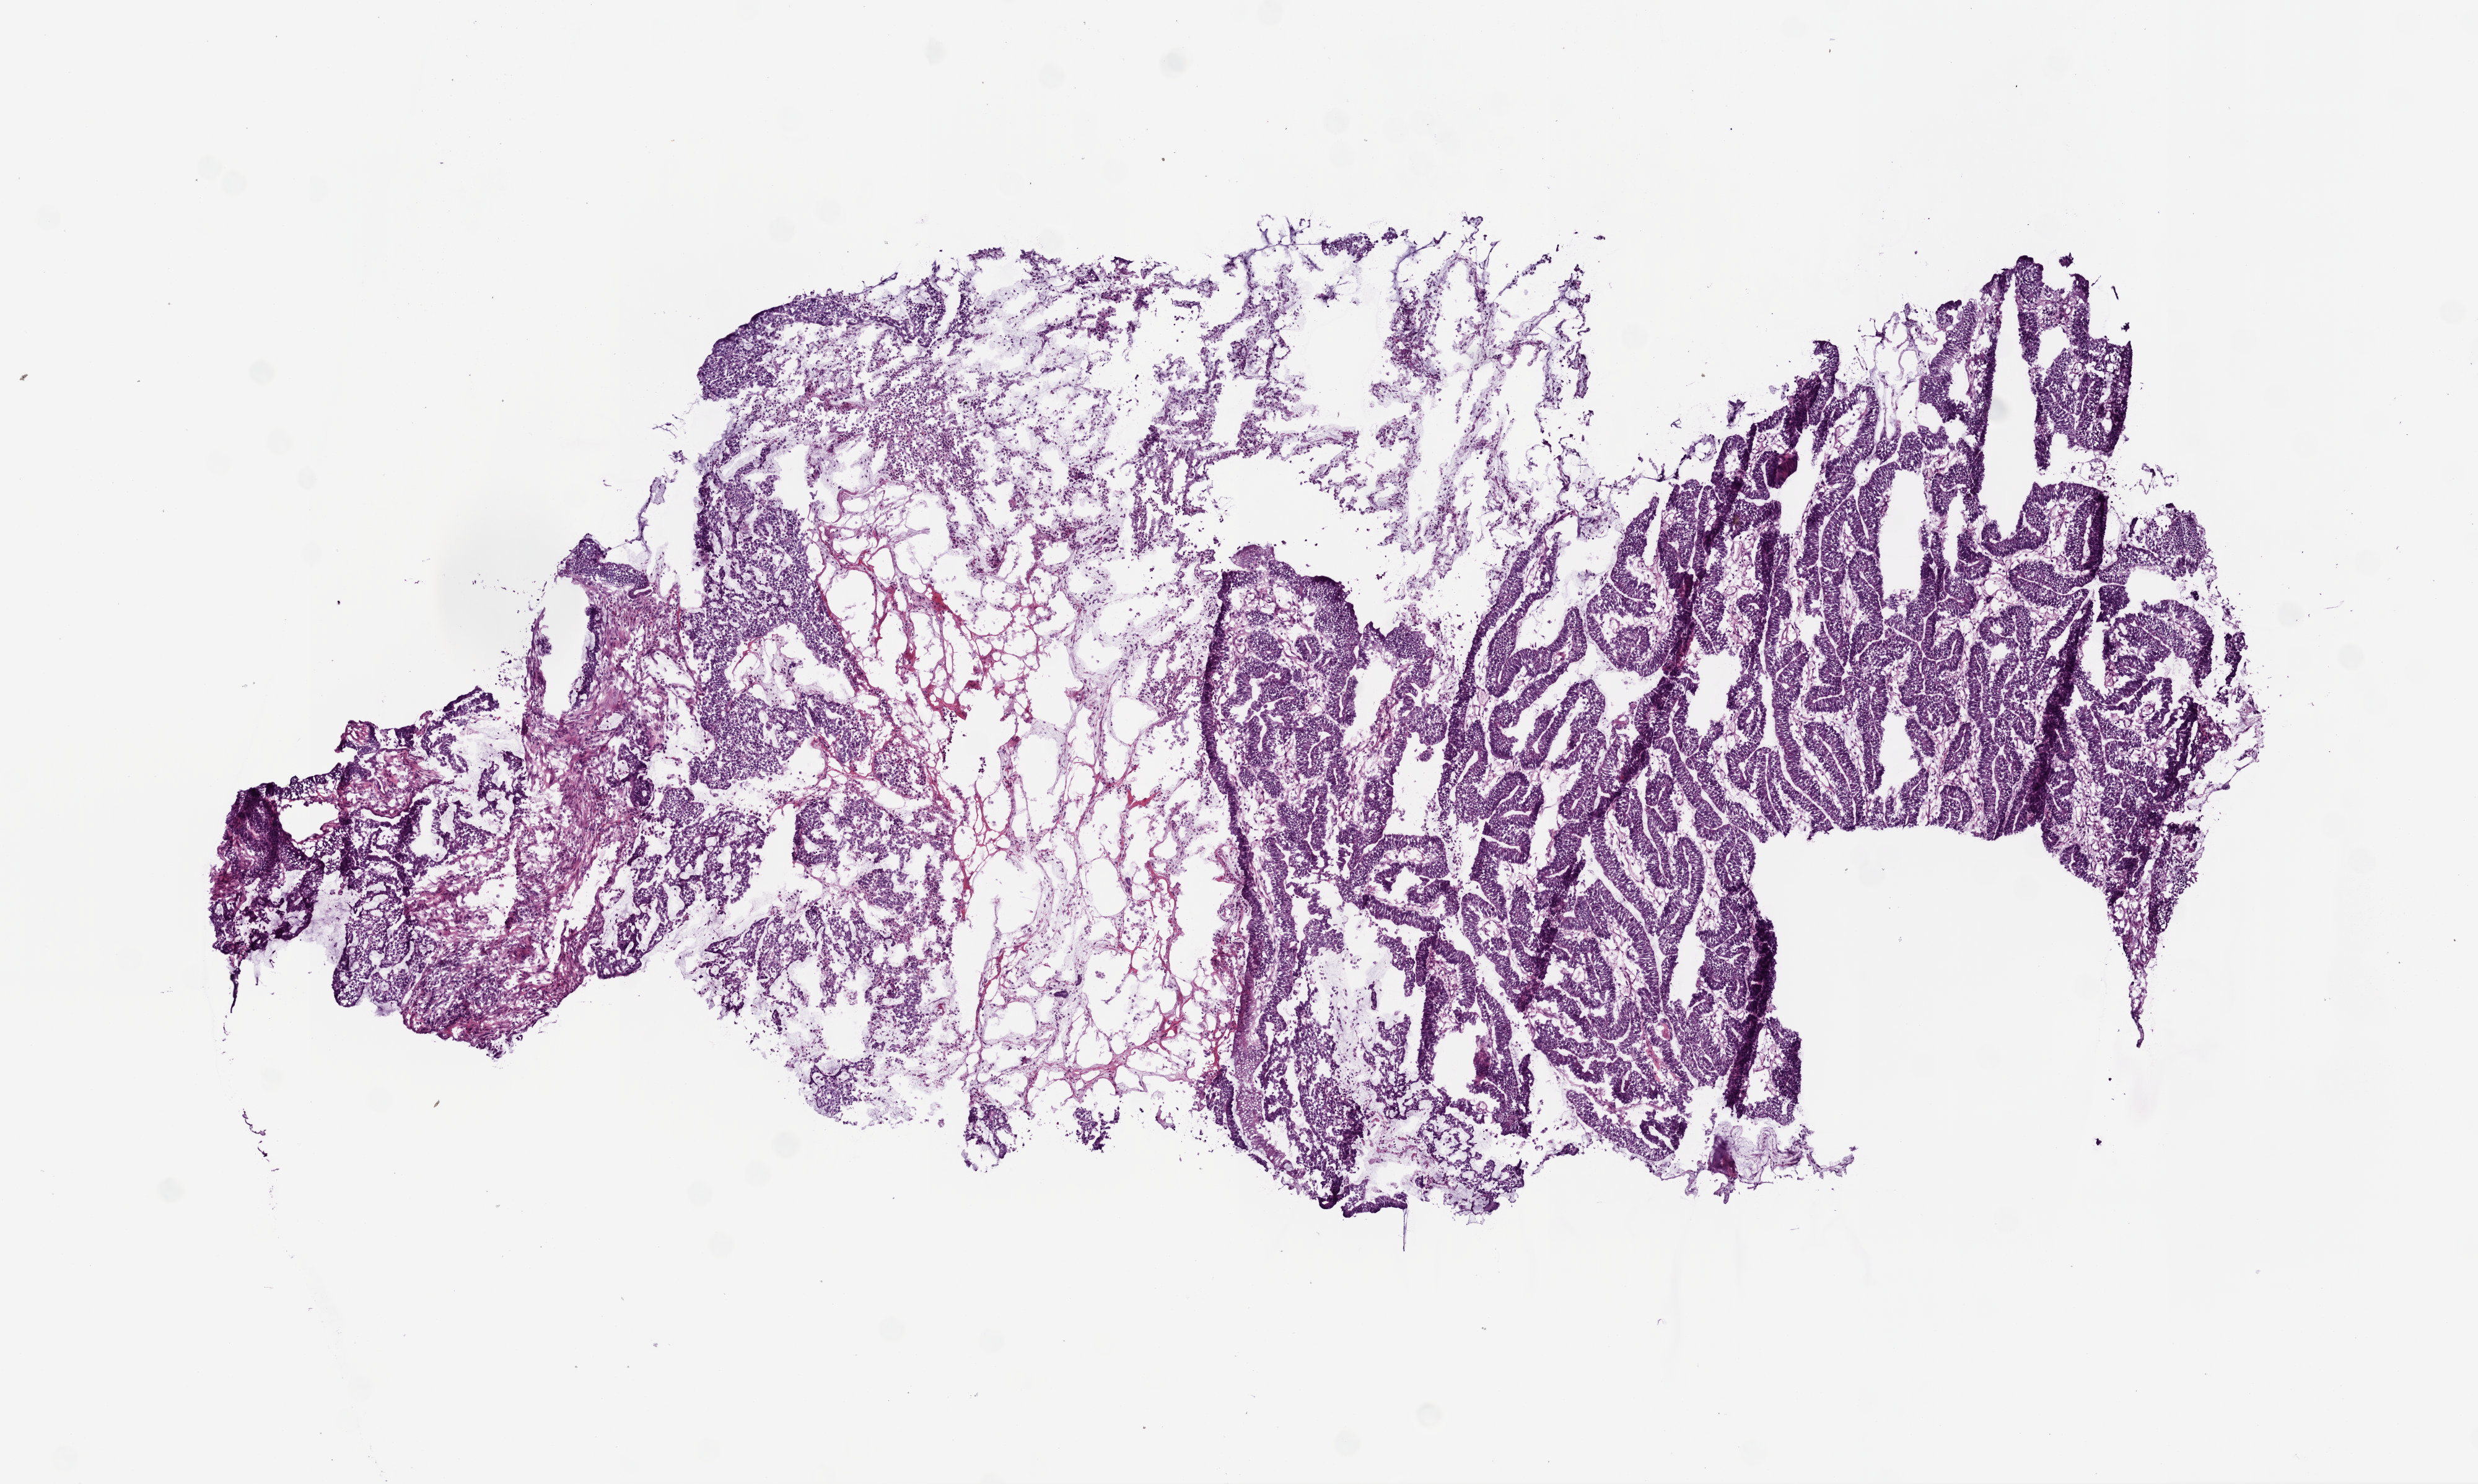
Whole-slide histology image, H&E, shown as a low-resolution overview of the whole scanned area (about 8.0 x 4.8 mm, acquisition: 20x scan), frozen section, colon, primary tumour sample. Patient: female, age at initial diagnosis 48 years. Composition of this section per pathologist review: tumour cells 33%, tumour nuclei 40%, normal cells 50%, stromal cells 15%, necrosis 2%.
Pathologic diagnosis: Mucinous adenocarcinoma (ascending colon). TNM: T4 N2 M0. AJCC pathologic stage: IIIC (6th edition).